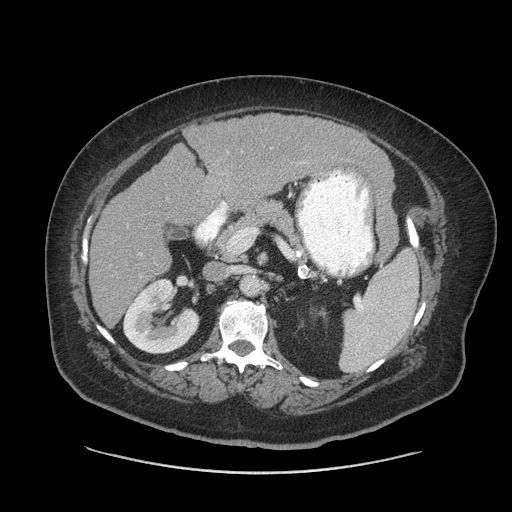
Contrast-enhanced abdominal CT (liver protocol), one axial slice; slice 36 of 91 in the series (ordered by position); 140 kVp; soft-tissue window (W 400 / L 40 HU); 2.5 mm slice thickness; 512 × 512 image matrix, field of view 420 × 420 mm. From the clinical record (not read from this slice): diagnosis: hepatocellular carcinoma (patient treated with transarterial chemoembolisation; whether this scan precedes or follows treatment is not stated here); TNM stage (as recorded): Stage-I; Child-Pugh class: A; tumour differentiation: well differentiated; tumour nodularity: uninodular.
Annotated regions visible in this slice (semi-automatic segmentation, software-assisted and operator-edited):
- liver parenchyma outside the tumour (the mass and vessels are separate outlines, so this box may not span the whole liver): bounding box <90,114,390,326> (left, top, right, bottom; pixels)
- liver vessels: <140,201,226,255>